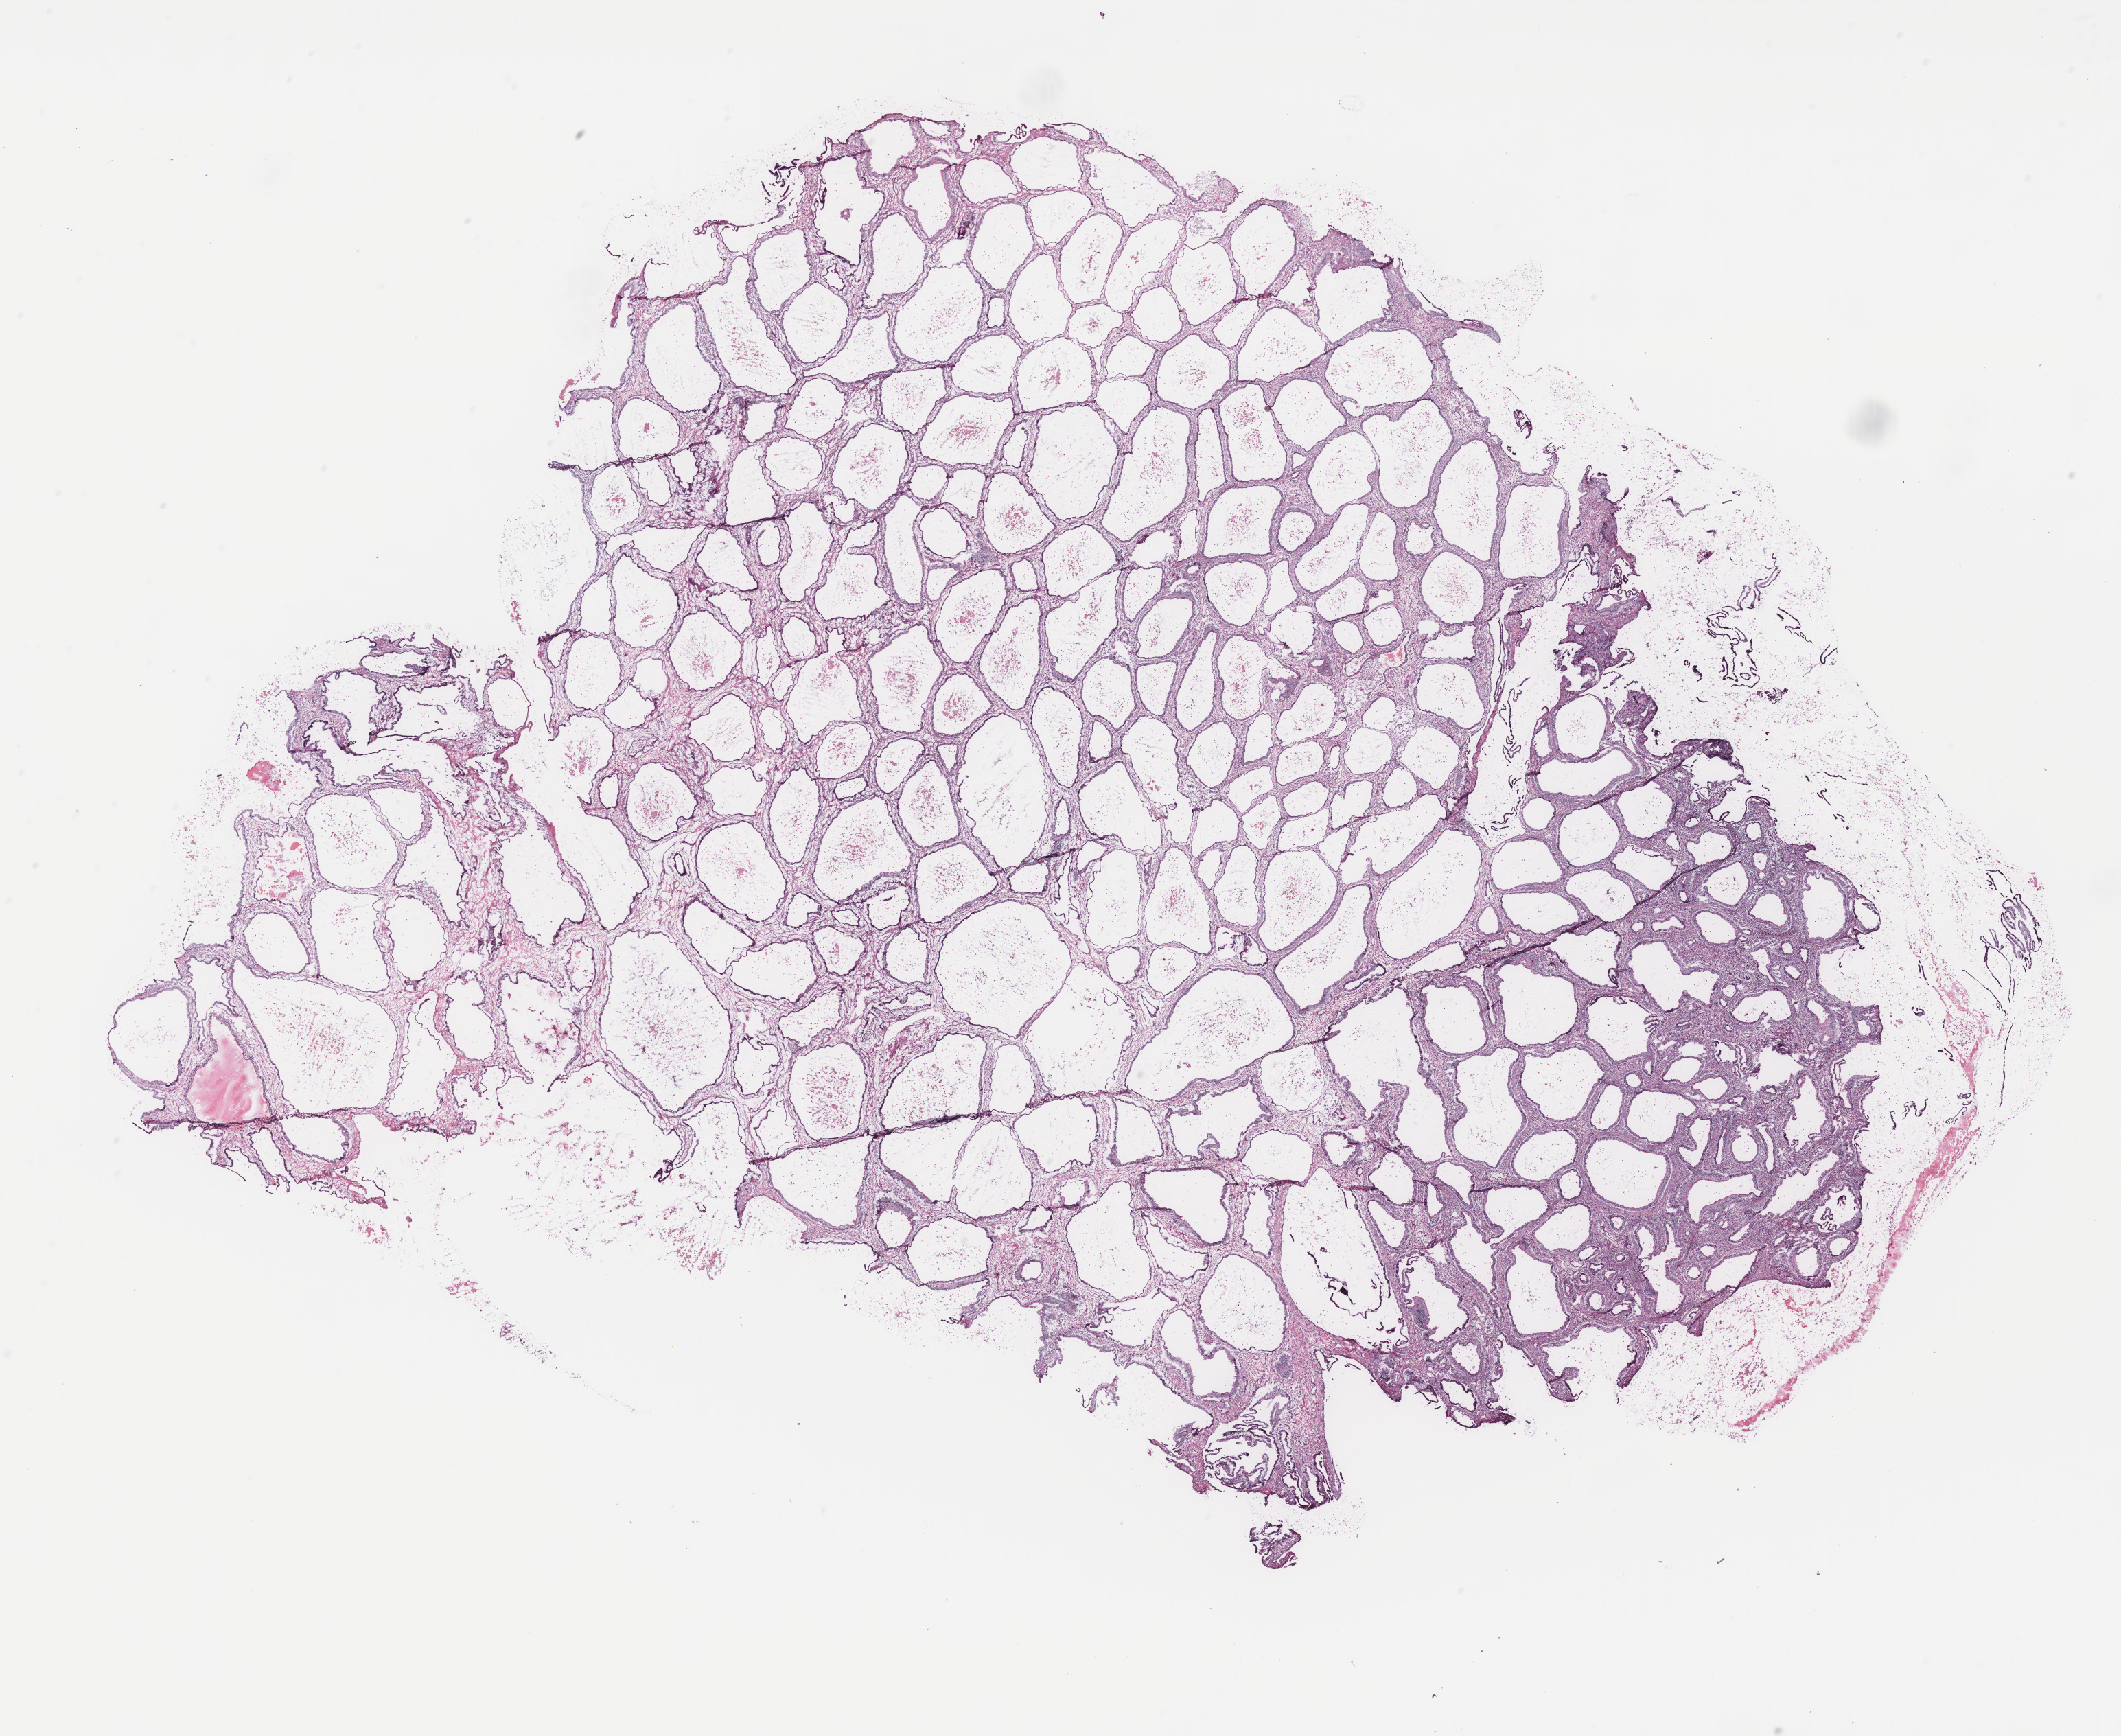
Whole-slide histology image, H&E — a low-resolution overview of the entire scanned area, about 24.7 x 20.2 mm. Tumour tissue sample, ovary. Patient: female, age 52 years.
Patient diagnosis (cohort enrolment): ovarian cancer (ovary).